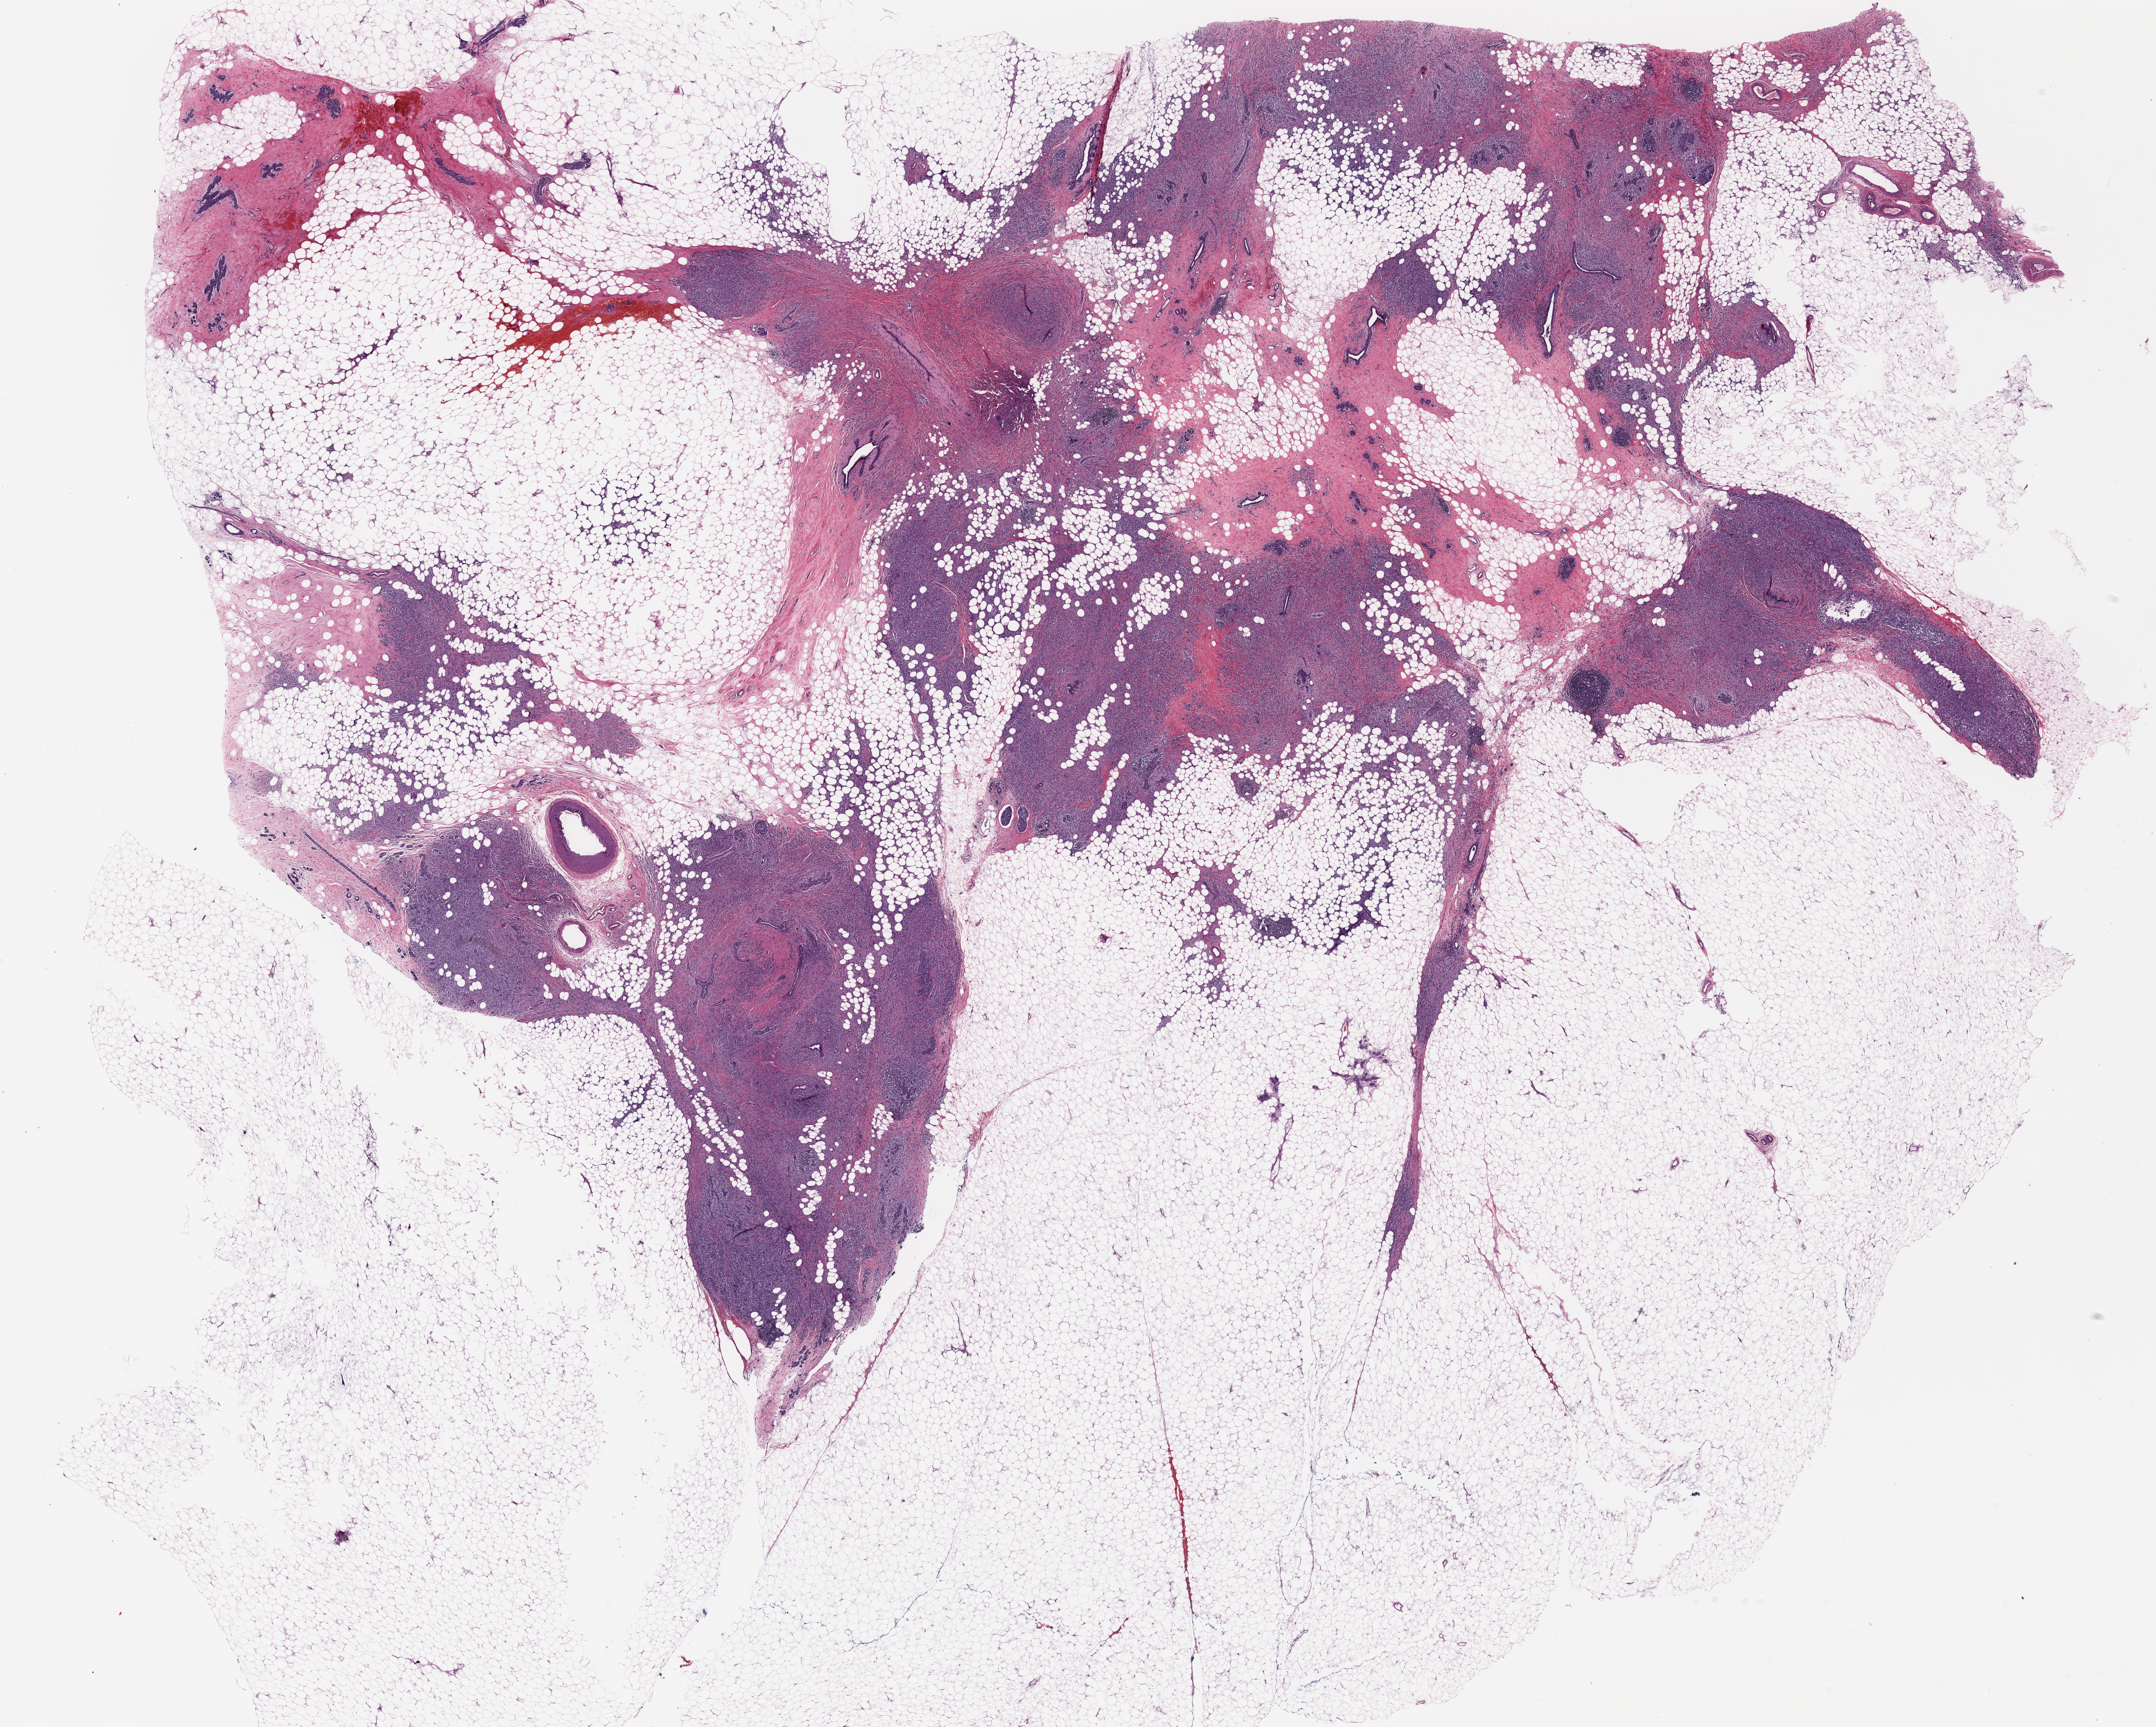
Whole-slide histology image, H&E, low-resolution overview of the scanned area, about 27.8 x 22.3 mm; formalin-fixed paraffin-embedded (FFPE) diagnostic section; sample: primary tumour, breast. Female, age 54 years at initial diagnosis.
AJCC pathologic stage: IIB. Pathologic diagnosis: Lobular carcinoma, NOS. Lymph nodes positive (case pathology): 2 of 44 examined. TNM: T2 N1a M0.